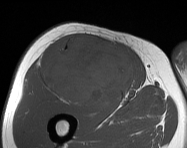
MRI of an extremity soft-tissue mass, one axial slice; position 88 of 114 along the scan axis; MR volume resampled by the dataset authors to the PET/CT grid (not the native acquisition matrix); 3.27 mm slice thickness; 187 × 148 image matrix, field of view 183 × 145 mm. Male patient. From the clinical record (not read from this slice): histological type: pleiomorphic leiomyosarcoma; grade: intermediate; site of the primary tumour: right thigh.
Outlined on this slice (expert contour drawn on MRI and transferred to this co-registered scan by the dataset authors):
- gross tumour volume including surrounding oedema: box from (x=43, y=36) to (x=135, y=105) px
- gross tumour volume (mass): (x=43, y=36)–(x=135, y=105)